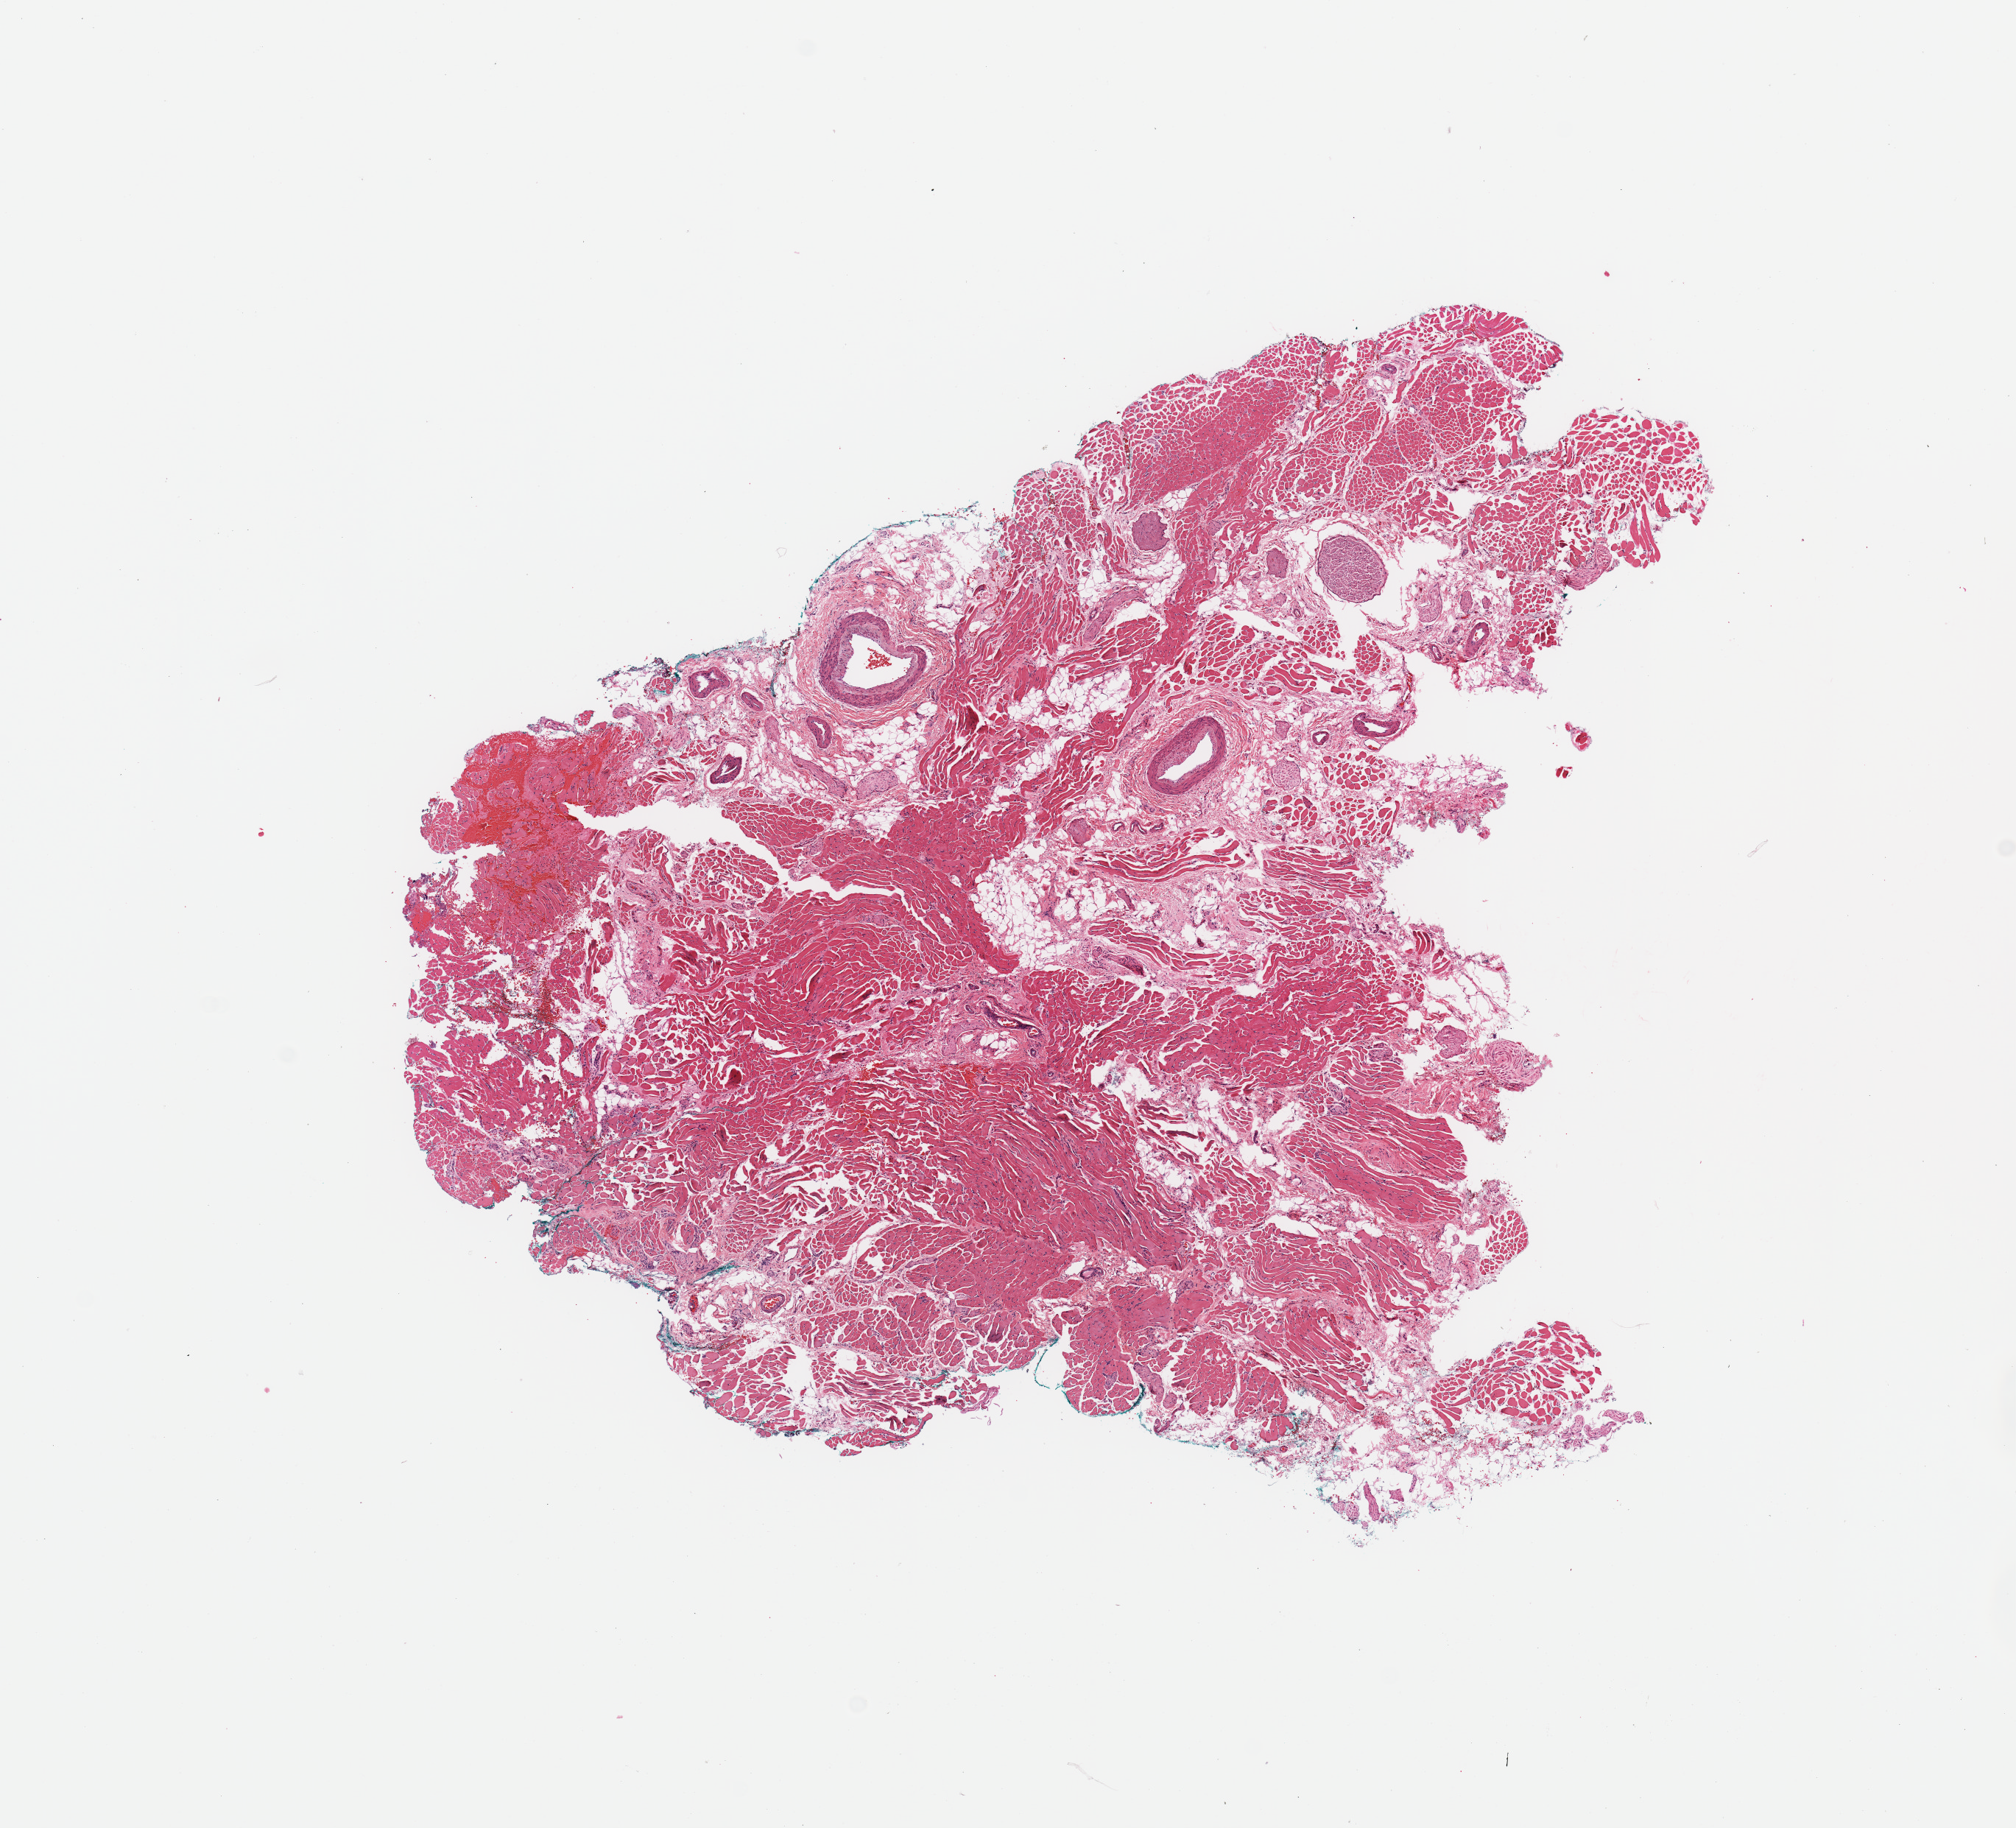
Whole-slide histology image, Hematoxylin and eosin (H&E) stained, low-resolution overview of the scanned area, about 10.8 x 9.8 mm (from a 20x scan); head and neck, tissue type not recorded. Patient: male, age 61 years.
Patient diagnosis: Squamous cell carcinoma, NOS (tongue, NOS).